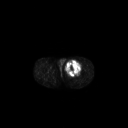
FDG PET of an extremity soft-tissue mass (from a PET/CT study), one axial slice. Position 249 of 267 along the scan axis. 128 × 128 image matrix. Male patient, age 63 years. From the clinical record (not read from this slice): histological type: pleiomorphic liposarcoma; grade: high; site of the primary tumour: left thigh.
Outlined on this slice (expert contour drawn on MRI and transferred to this co-registered scan by the dataset authors):
- gross tumour volume including surrounding oedema: box from (x=65, y=60) to (x=82, y=75) px
- gross tumour volume (mass): (x=65, y=60)–(x=82, y=75)